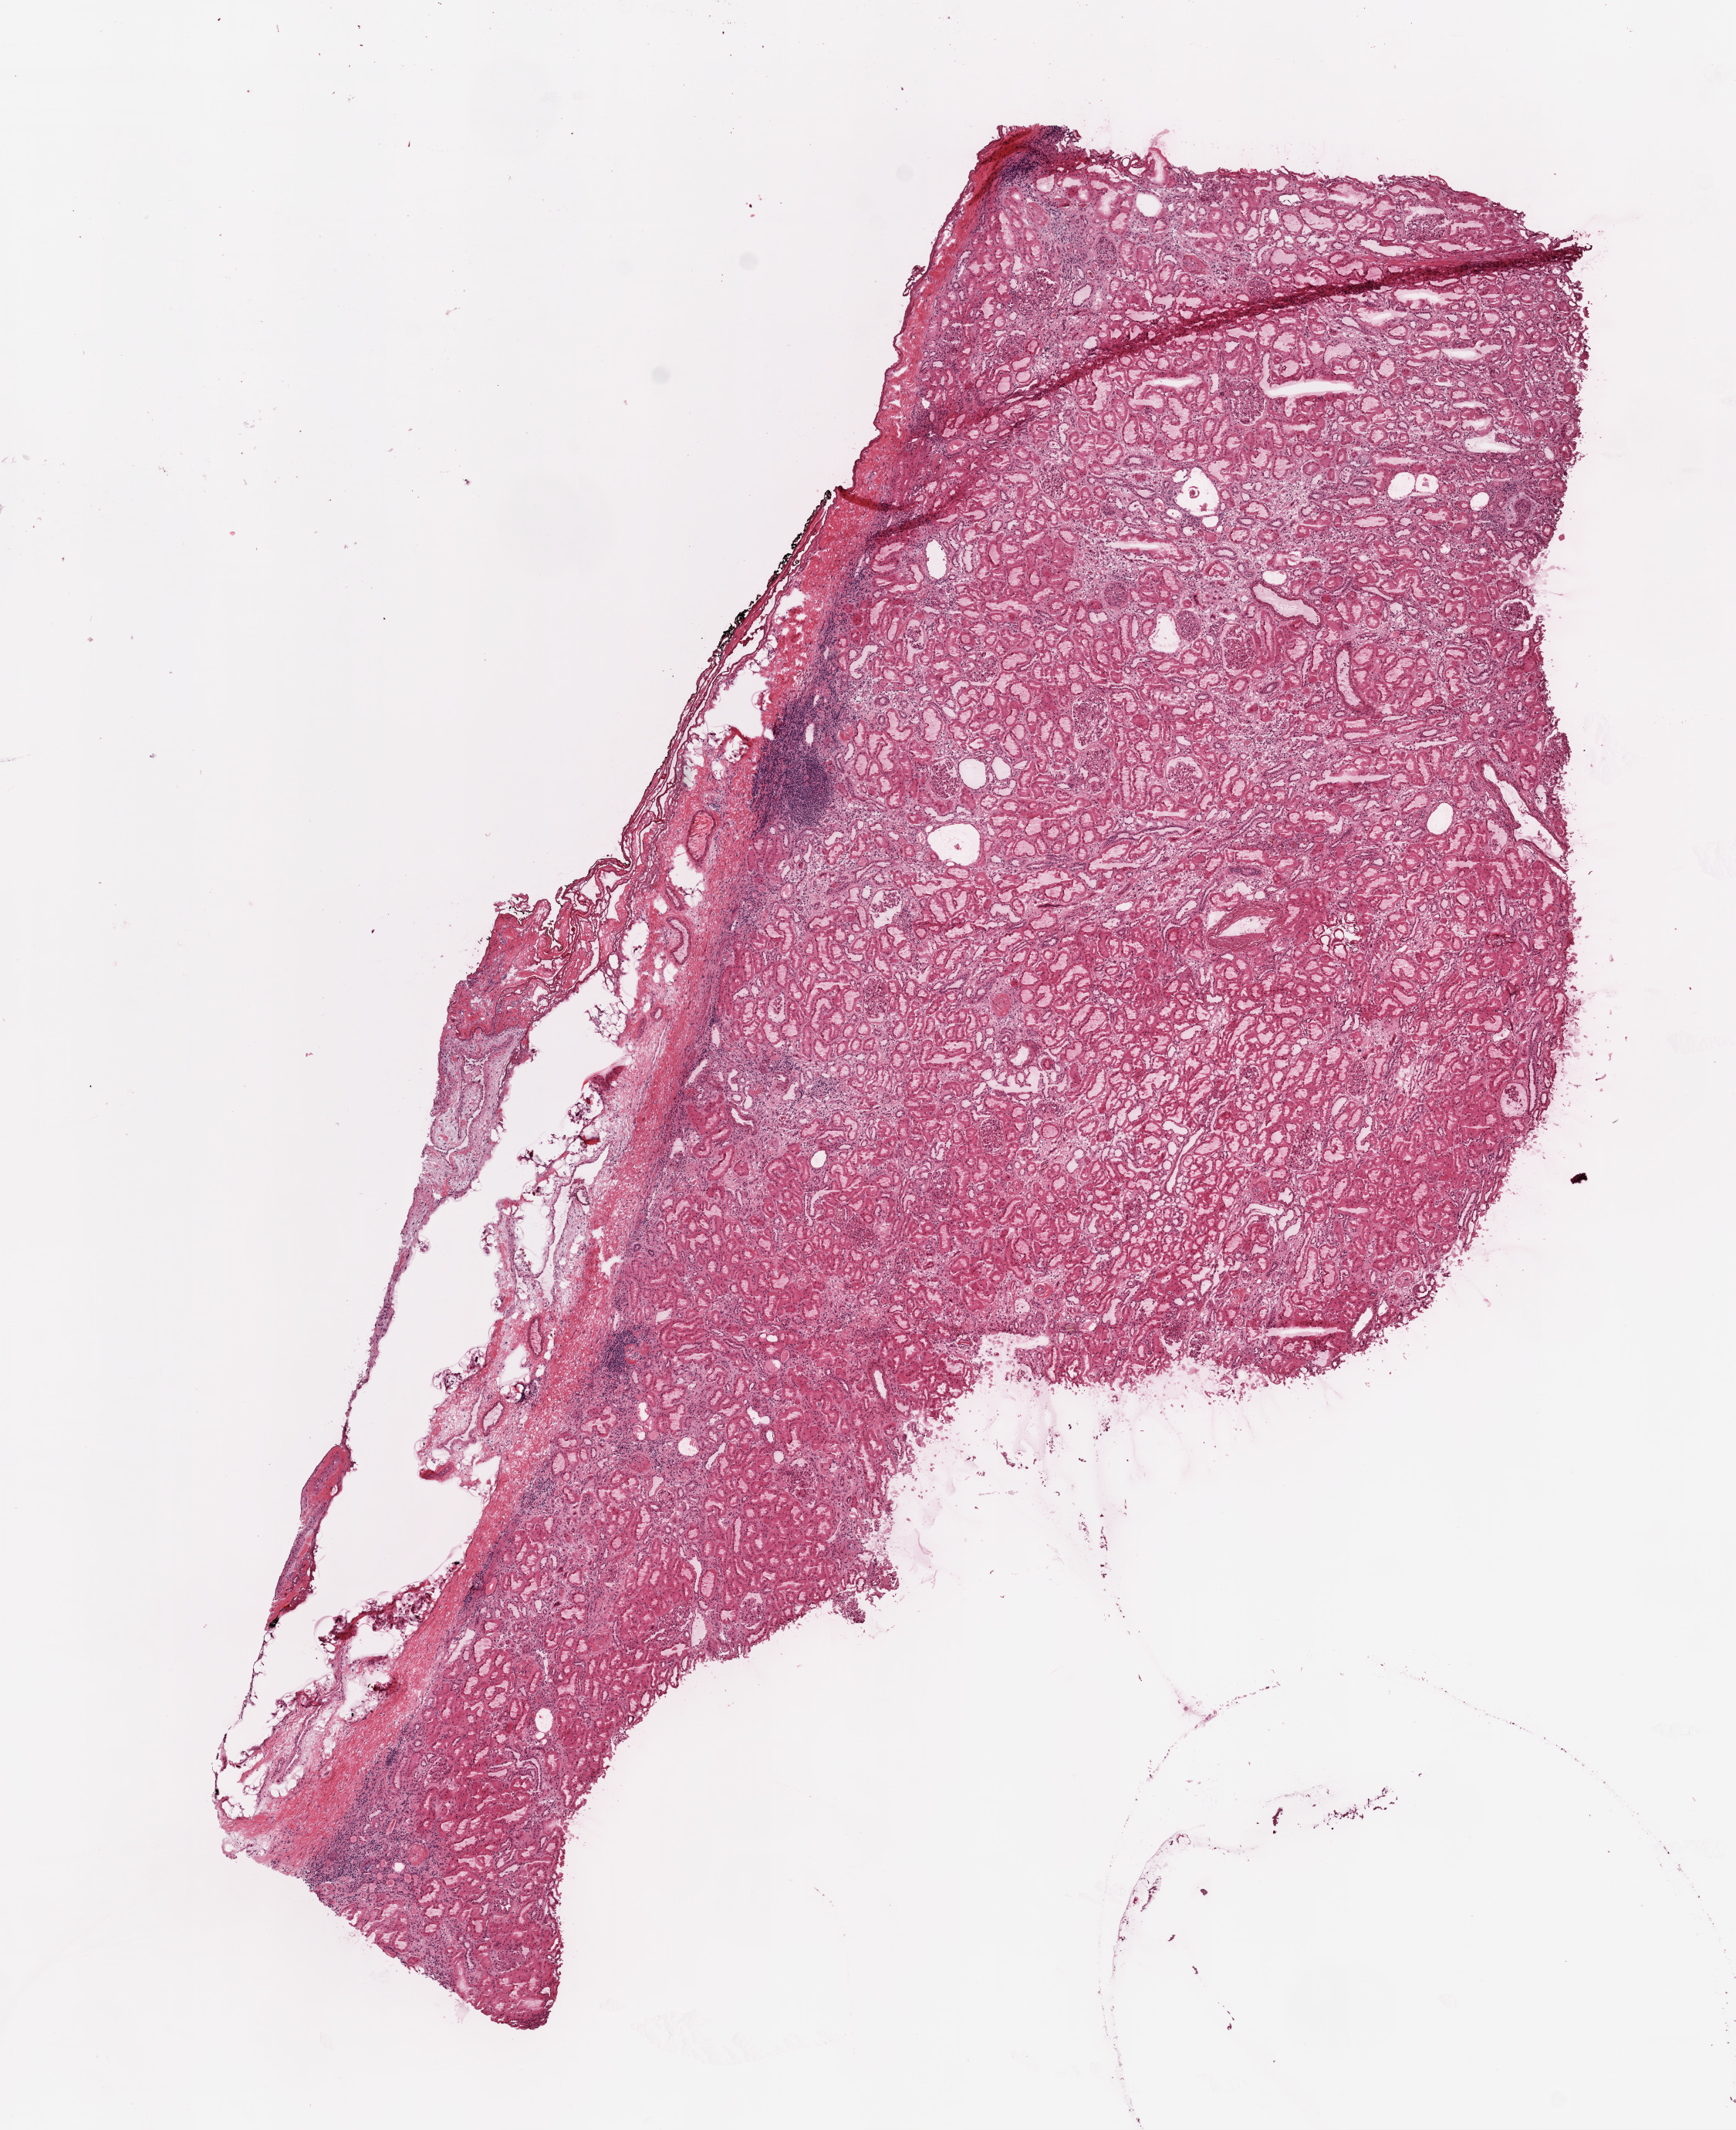
Whole-slide histology image, Hematoxylin and eosin (H&E) stained, a low-resolution overview of the entire scanned area, about 9.0 x 11.1 mm (from a 20x scan); frozen section; sample: solid tissue normal (non-tumour tissue), kidney. Female patient; age at initial diagnosis 73 years.
- this section: solid tissue normal (non-tumour) sample from the same patient
- patient diagnosis: Clear cell adenocarcinoma, NOS